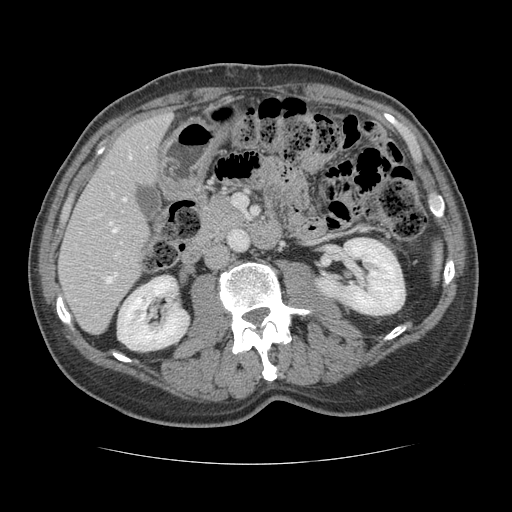
Contrast-enhanced abdominal CT, one axial slice. Slice 55 of 134 in the series (ordered by position). Reconstruction kernel STANDARD. 120 kVp. Intravenous contrast given. Soft-tissue window (W 400 / L 40 HU). 512 × 512 image matrix, field of view 377 × 377 mm. Male patient, age 68 years. Case-level facts recorded for this patient, not image findings: diagnosis: colorectal cancer liver metastases, imaged before liver resection.
Annotated regions visible in this slice (expert manual segmentation):
- hepatic veins: bounding box [x1, y1, x2, y2] px = [109, 156, 132, 232]
- liver: [60, 114, 170, 334]
- planned liver remnant (the part of the liver to remain after resection): [60, 114, 170, 333]
- portal vein (with intrahepatic branches): [106, 272, 117, 283]